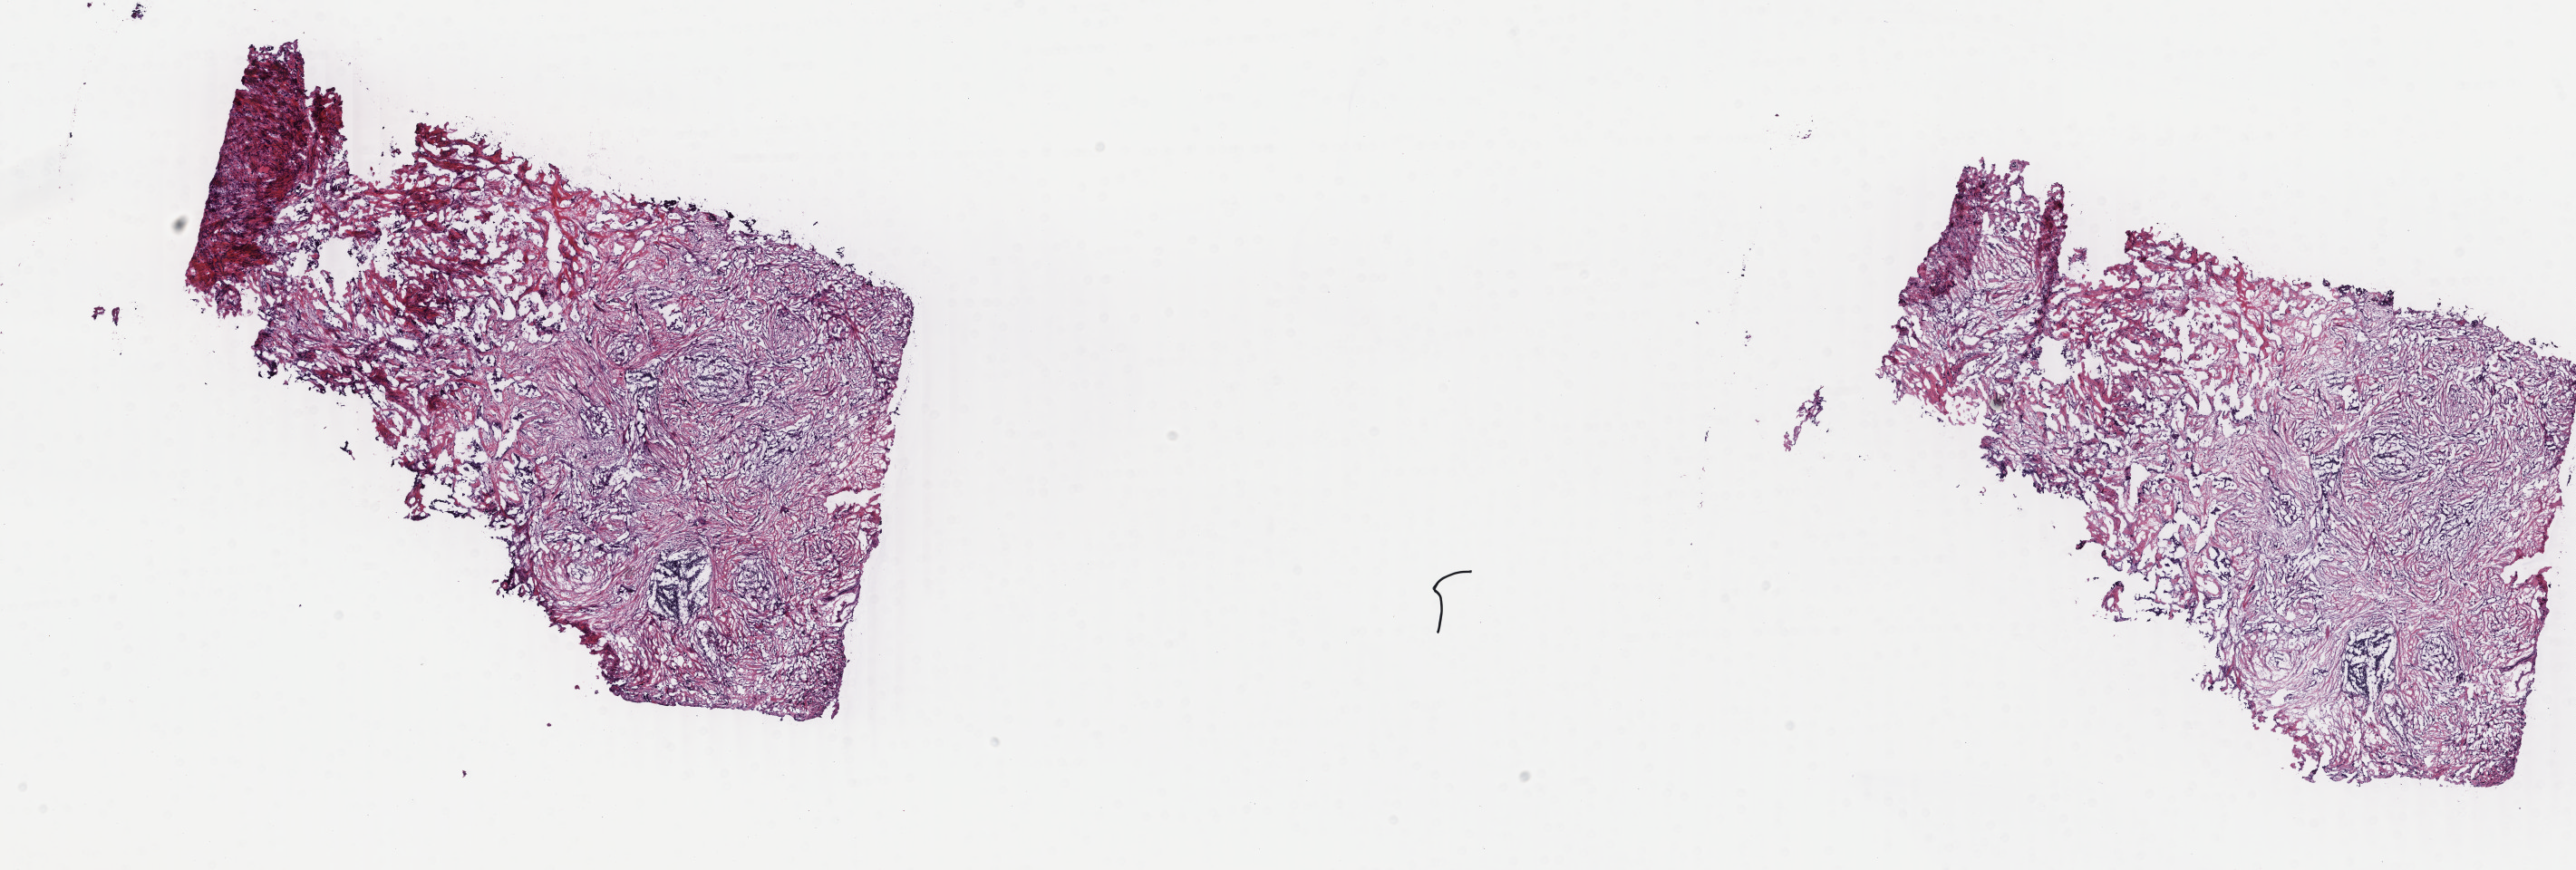
Digitized Hematoxylin and eosin (H&E) stained tissue section (whole slide) — shown as a low-resolution overview of the whole scanned area (about 22.6 x 7.6 mm, slide scanned at 40x), frozen section from the top of the tissue portion, breast, primary tumour sample. Female, age 40 years at initial diagnosis. Pathologist review of this section (percent, as recorded): tumour cells 75%, tumour nuclei 75%, normal cells 0%, stromal cells 25%, necrosis 0%. Inflammatory infiltration, as recorded: lymphocyte infiltration 5%, monocyte infiltration 1%, neutrophil infiltration 1%.
* TNM: T3 N1b M0
* diagnosis: Lobular carcinoma, NOS
* AJCC pathologic stage: IIIA